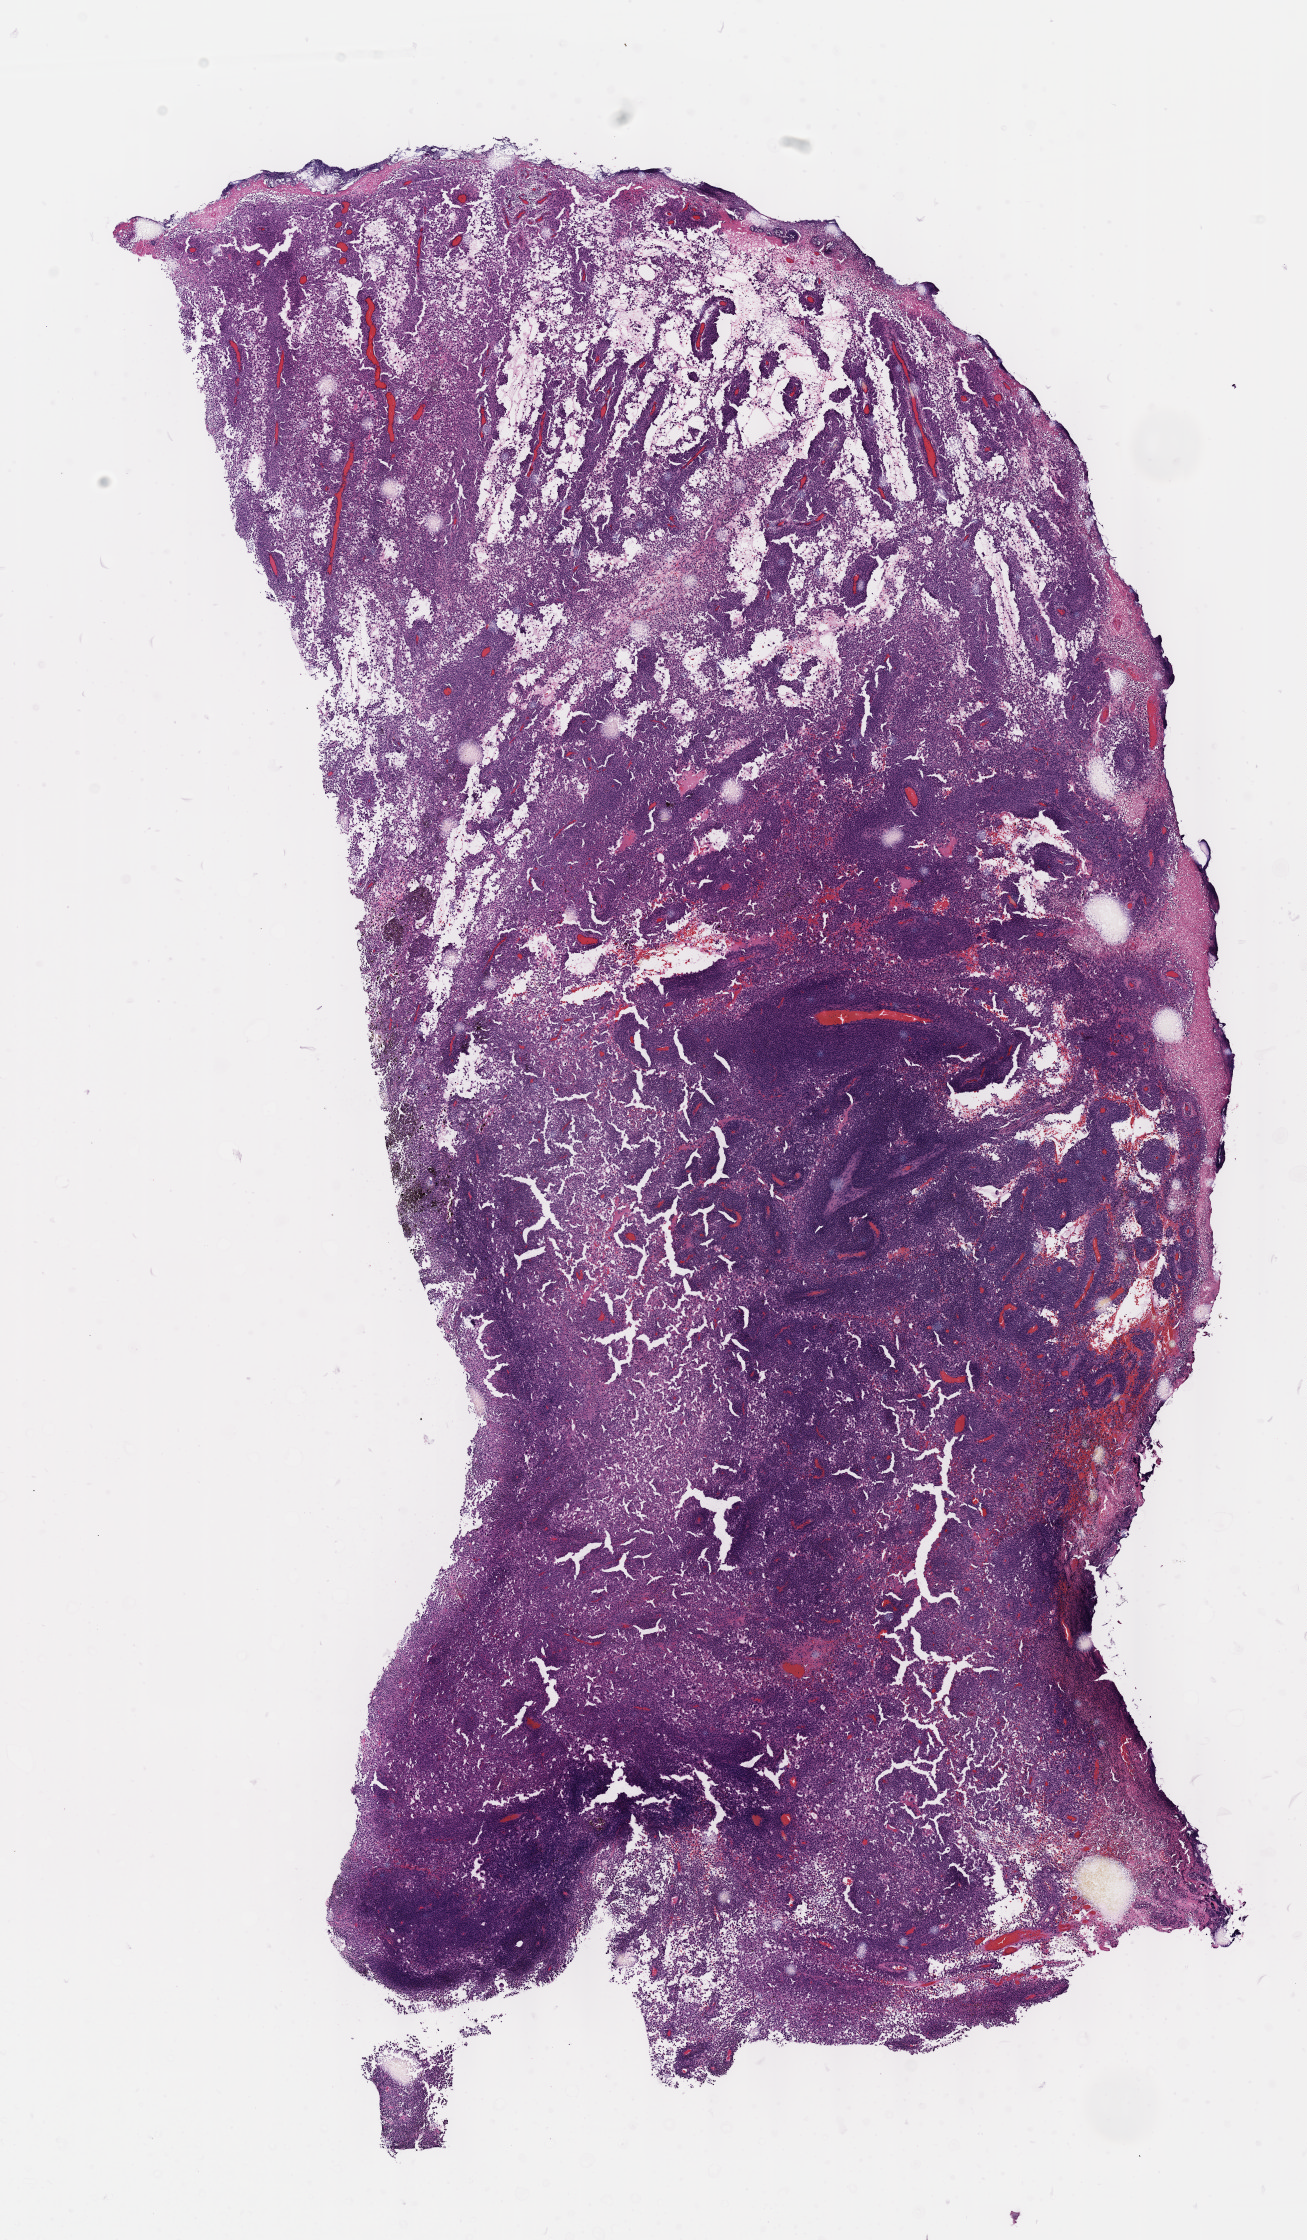
Whole-slide histology image, H&E-stained, low-resolution overview of the scanned area, about 10.6 x 18.1 mm (slide scanned at 40x). Formalin-fixed paraffin-embedded (FFPE) diagnostic section. Primary tumour sample from the skin. Patient: male, age at initial diagnosis 83 years.
Pathologic diagnosis: Epithelioid cell melanoma. AJCC pathologic stage: IIC (7th edition).